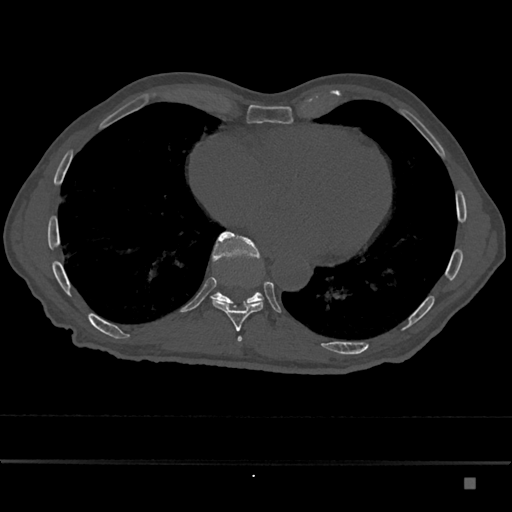
CT including the spine, one axial slice; slice 783 of 797 in the series (ordered by position); reconstruction kernel Br40s/3; 120 kVp; bone window (W 1800 / L 400 HU); 0.5 mm slice thickness; 512 × 512 image matrix, field of view 390 × 390 mm. Male patient, age 72 years. Case-level facts recorded for this patient, not image findings: primary cancer: prostate.
Annotated regions visible in this slice (semi-automatic segmentation, software-assisted and operator-edited):
- T10 vertebra: bounding box <210,232,264,307> (left, top, right, bottom; pixels)
- T9 vertebra: <212,300,264,332>